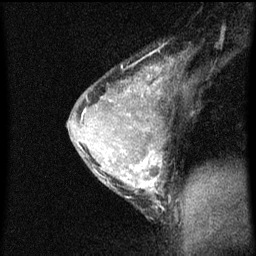
Breast MRI (dynamic contrast-enhanced), one sagittal slice. Position 43 of 60 along the scan axis. Dynamic contrast-enhanced series, image 2 of 3 at this slice position (ordered by acquisition). 1.5 T. TE 4.2 ms, TR 8 ms. 2 mm slice thickness. 256 × 256 image matrix. Female patient, age 33 years.
Annotated regions visible in this slice (semi-automatic segmentation, software-assisted and operator-edited):
- analysis volume of interest (the breast-tissue region the enhancement analysis was run in; not a lesion): bounding box (x1, y1, x2, y2) in pixels: (67, 58, 183, 209)
- tumour enhancement mask (voxels above the 70 % enhancement threshold inside the analysis volume of interest): (82, 66, 164, 209)